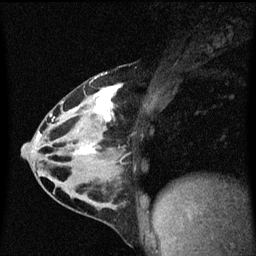
Breast MRI (dynamic contrast-enhanced), one sagittal slice. Position 29 of 60 along the scan axis. Dynamic contrast-enhanced series, image 2 of 3 at this slice position (ordered by acquisition). 1.5 T. TE 4.2 ms, TR 8.4 ms. 2 mm slice thickness. 256 × 256 image matrix. Female patient, age 32 years.
Structures marked on this image (semi-automatically segmented with operator editing):
- analysis volume of interest (the breast-tissue region the enhancement analysis was run in; not a lesion): box from (x=34, y=74) to (x=124, y=169) px
- tumour enhancement mask (voxels above the 70 % enhancement threshold inside the analysis volume of interest): (x=50, y=84)–(x=122, y=155)